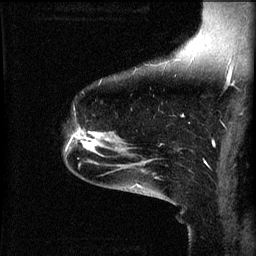
Breast MRI (dynamic contrast-enhanced), one sagittal slice; position 42 of 60 along the scan axis; 3 images stored at this slice position (order not interpretable as contrast timing); 1.5 T; TE 4.2 ms, TR 8.2 ms; 2 mm slice thickness; 256 × 256 image matrix, field of view 200 × 200 mm. Patient: female, 49 years.
Annotated regions visible in this slice (semi-automatically segmented with operator editing):
- analysis volume of interest (the breast-tissue region the enhancement analysis was run in; not a lesion): bounding box [x1, y1, x2, y2] px = [66, 128, 113, 159]
- tumour enhancement mask (voxels above the 70 % enhancement threshold inside the analysis volume of interest): [66, 130, 111, 155]